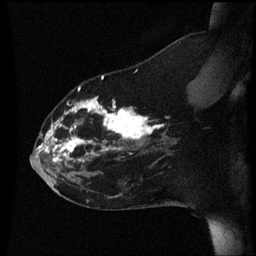
Breast MRI (dynamic contrast-enhanced), one sagittal slice; position 19 of 60 along the scan axis; dynamic contrast-enhanced series, image 2 of 3 at this slice position (ordered by acquisition); 1.5 T; TE 4.2 ms, TR 8.4 ms; 256 × 256 image matrix. Patient: female, 35 years. Case-level facts recorded for this patient, not image findings: setting: breast cancer imaged before/during neoadjuvant chemotherapy; receptor status: HER2-positive.
Outlined on this slice (semi-automatically segmented with operator editing):
- analysis volume of interest (the breast-tissue region the enhancement analysis was run in; not a lesion): bounding box (x1, y1, x2, y2) in pixels: (31, 72, 178, 173)
- tumour enhancement mask (voxels above the 70 % enhancement threshold inside the analysis volume of interest): (38, 76, 165, 163)